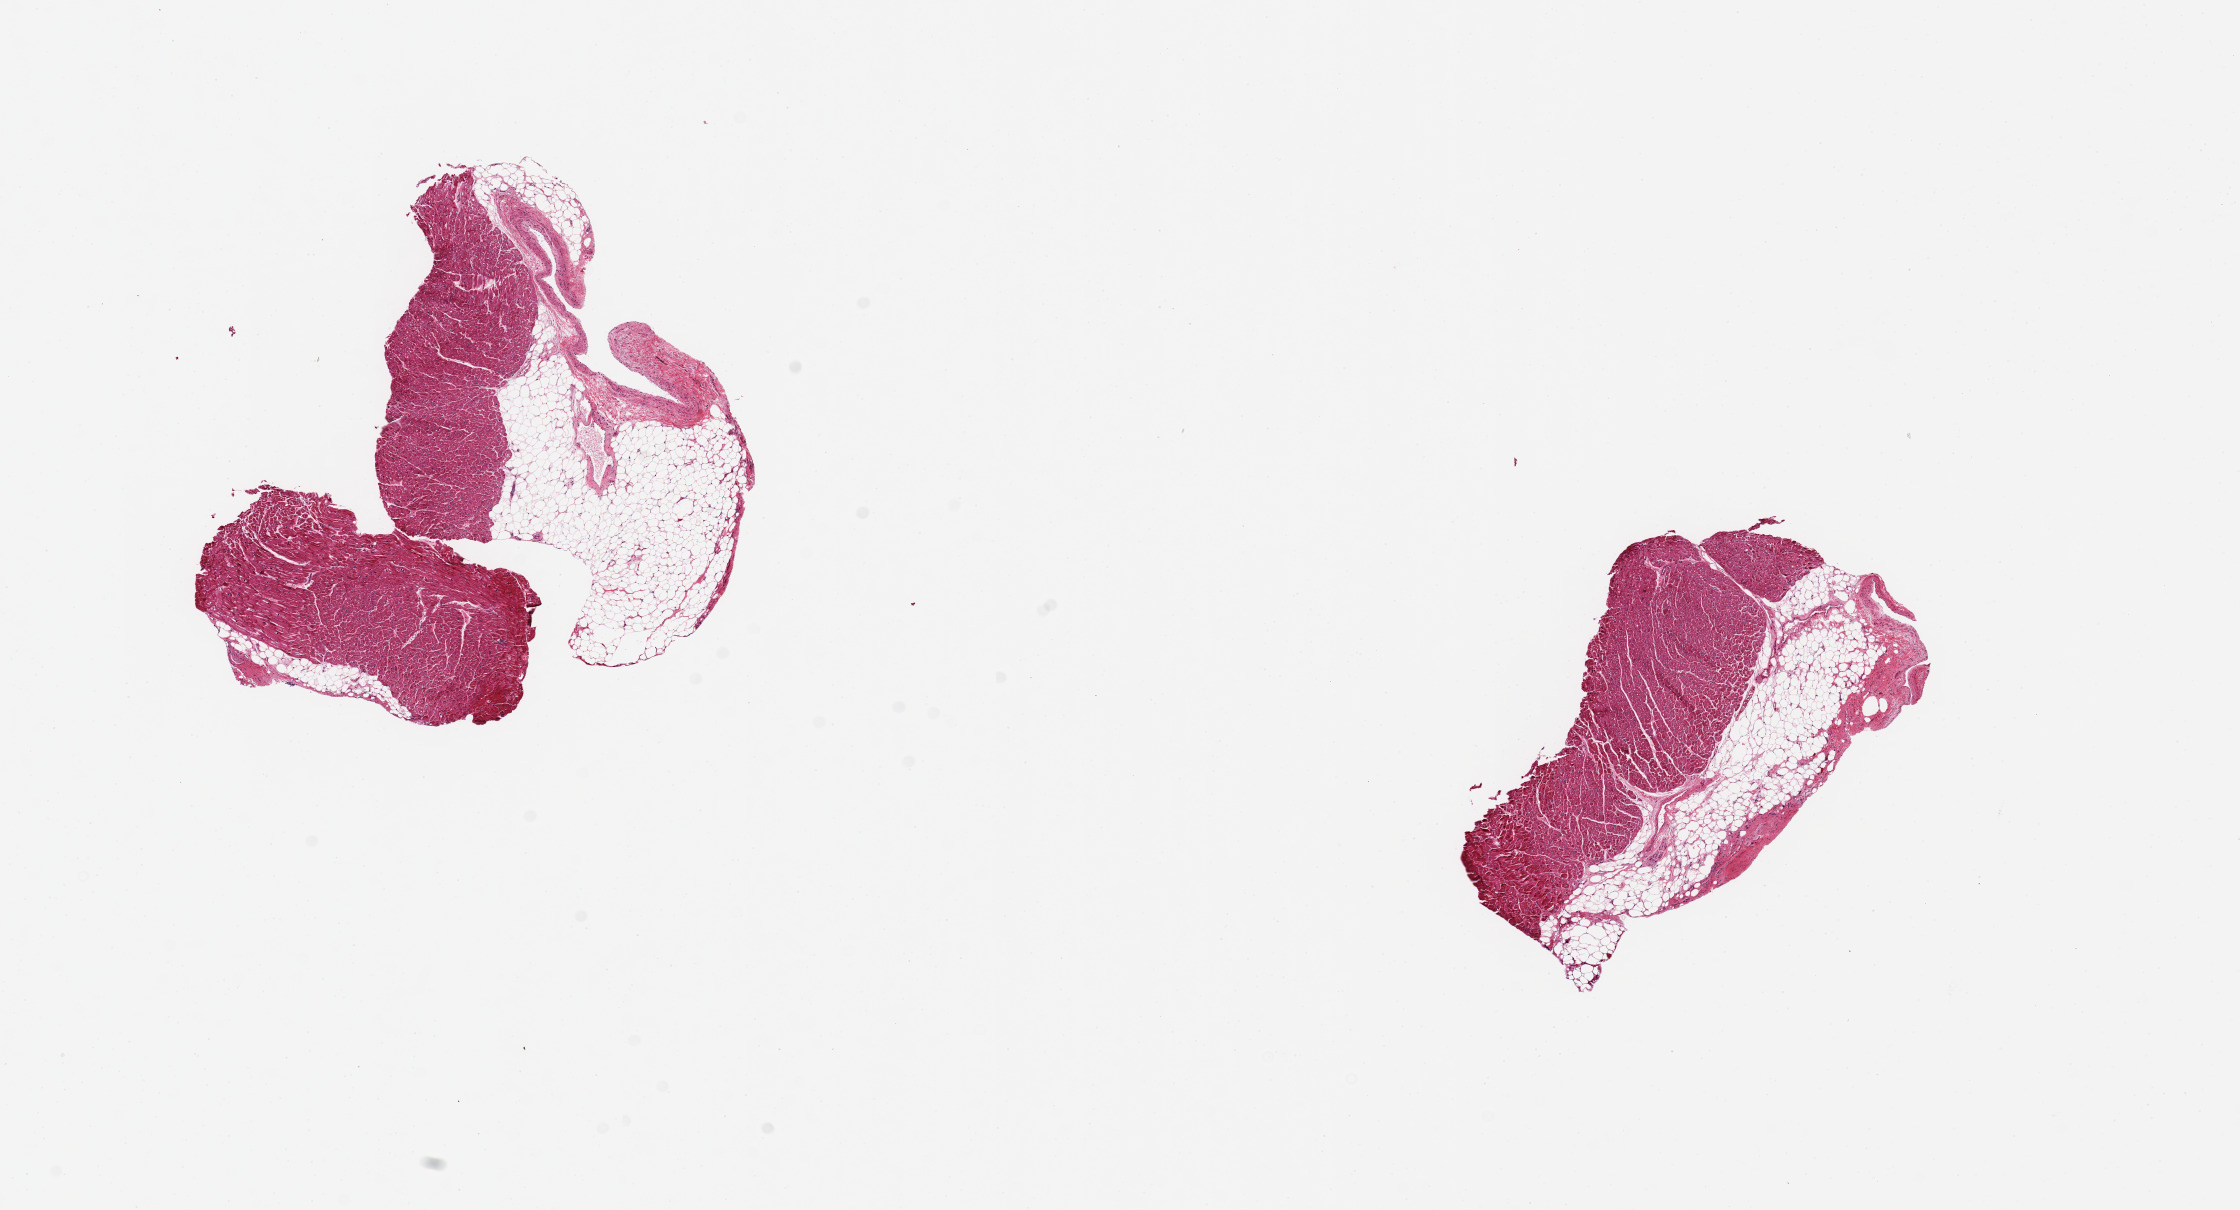
Whole-slide image, H&E stain, brightfield — shown as a low-resolution overview of the whole scanned area (about 17.7 x 9.6 mm); PAXgene-fixed paraffin-embedded (PFPE) section; section of coronary artery (target tissue); donor tissue sample. Donor sex: male.
Review note (as recorded): 2 pieces, 4x4 & 4x2.5mm; myocardium, vein and adipose tissue, NO ARTERY.